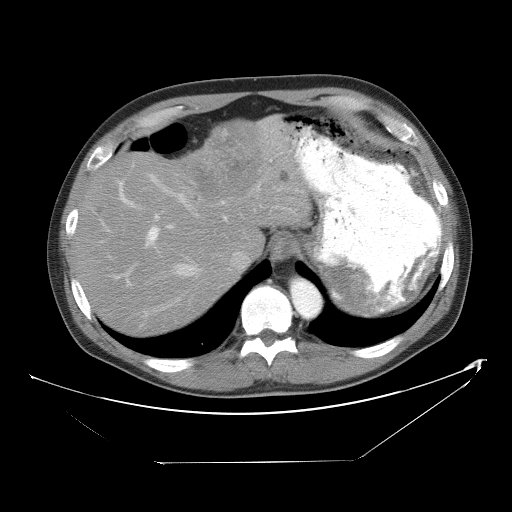
Contrast-enhanced abdominal CT, one axial slice. Slice 41 of 53 in the series (ordered by position). Reconstruction kernel STANDARD. Soft-tissue window (W 400 / L 40 HU). 5 mm slice thickness. 512 × 512 image matrix, field of view 438 × 438 mm. Male patient, age 59 years. Case-level facts recorded for this patient, not image findings: diagnosis: colorectal cancer liver metastases, imaged before liver resection; multiple liver metastases: yes; largest metastasis: 8.5 cm.
Structures marked on this image (manually delineated by an expert):
- hepatic veins: bounding box <148,174,256,312> (left, top, right, bottom; pixels)
- liver: <76,123,309,332>
- planned liver remnant (the part of the liver to remain after resection): <76,159,233,332>
- portal vein (with intrahepatic branches): <114,182,280,315>
- liver metastasis: <281,171,290,184>
- liver metastasis: <99,209,105,216>
- liver metastasis: <194,129,262,197>